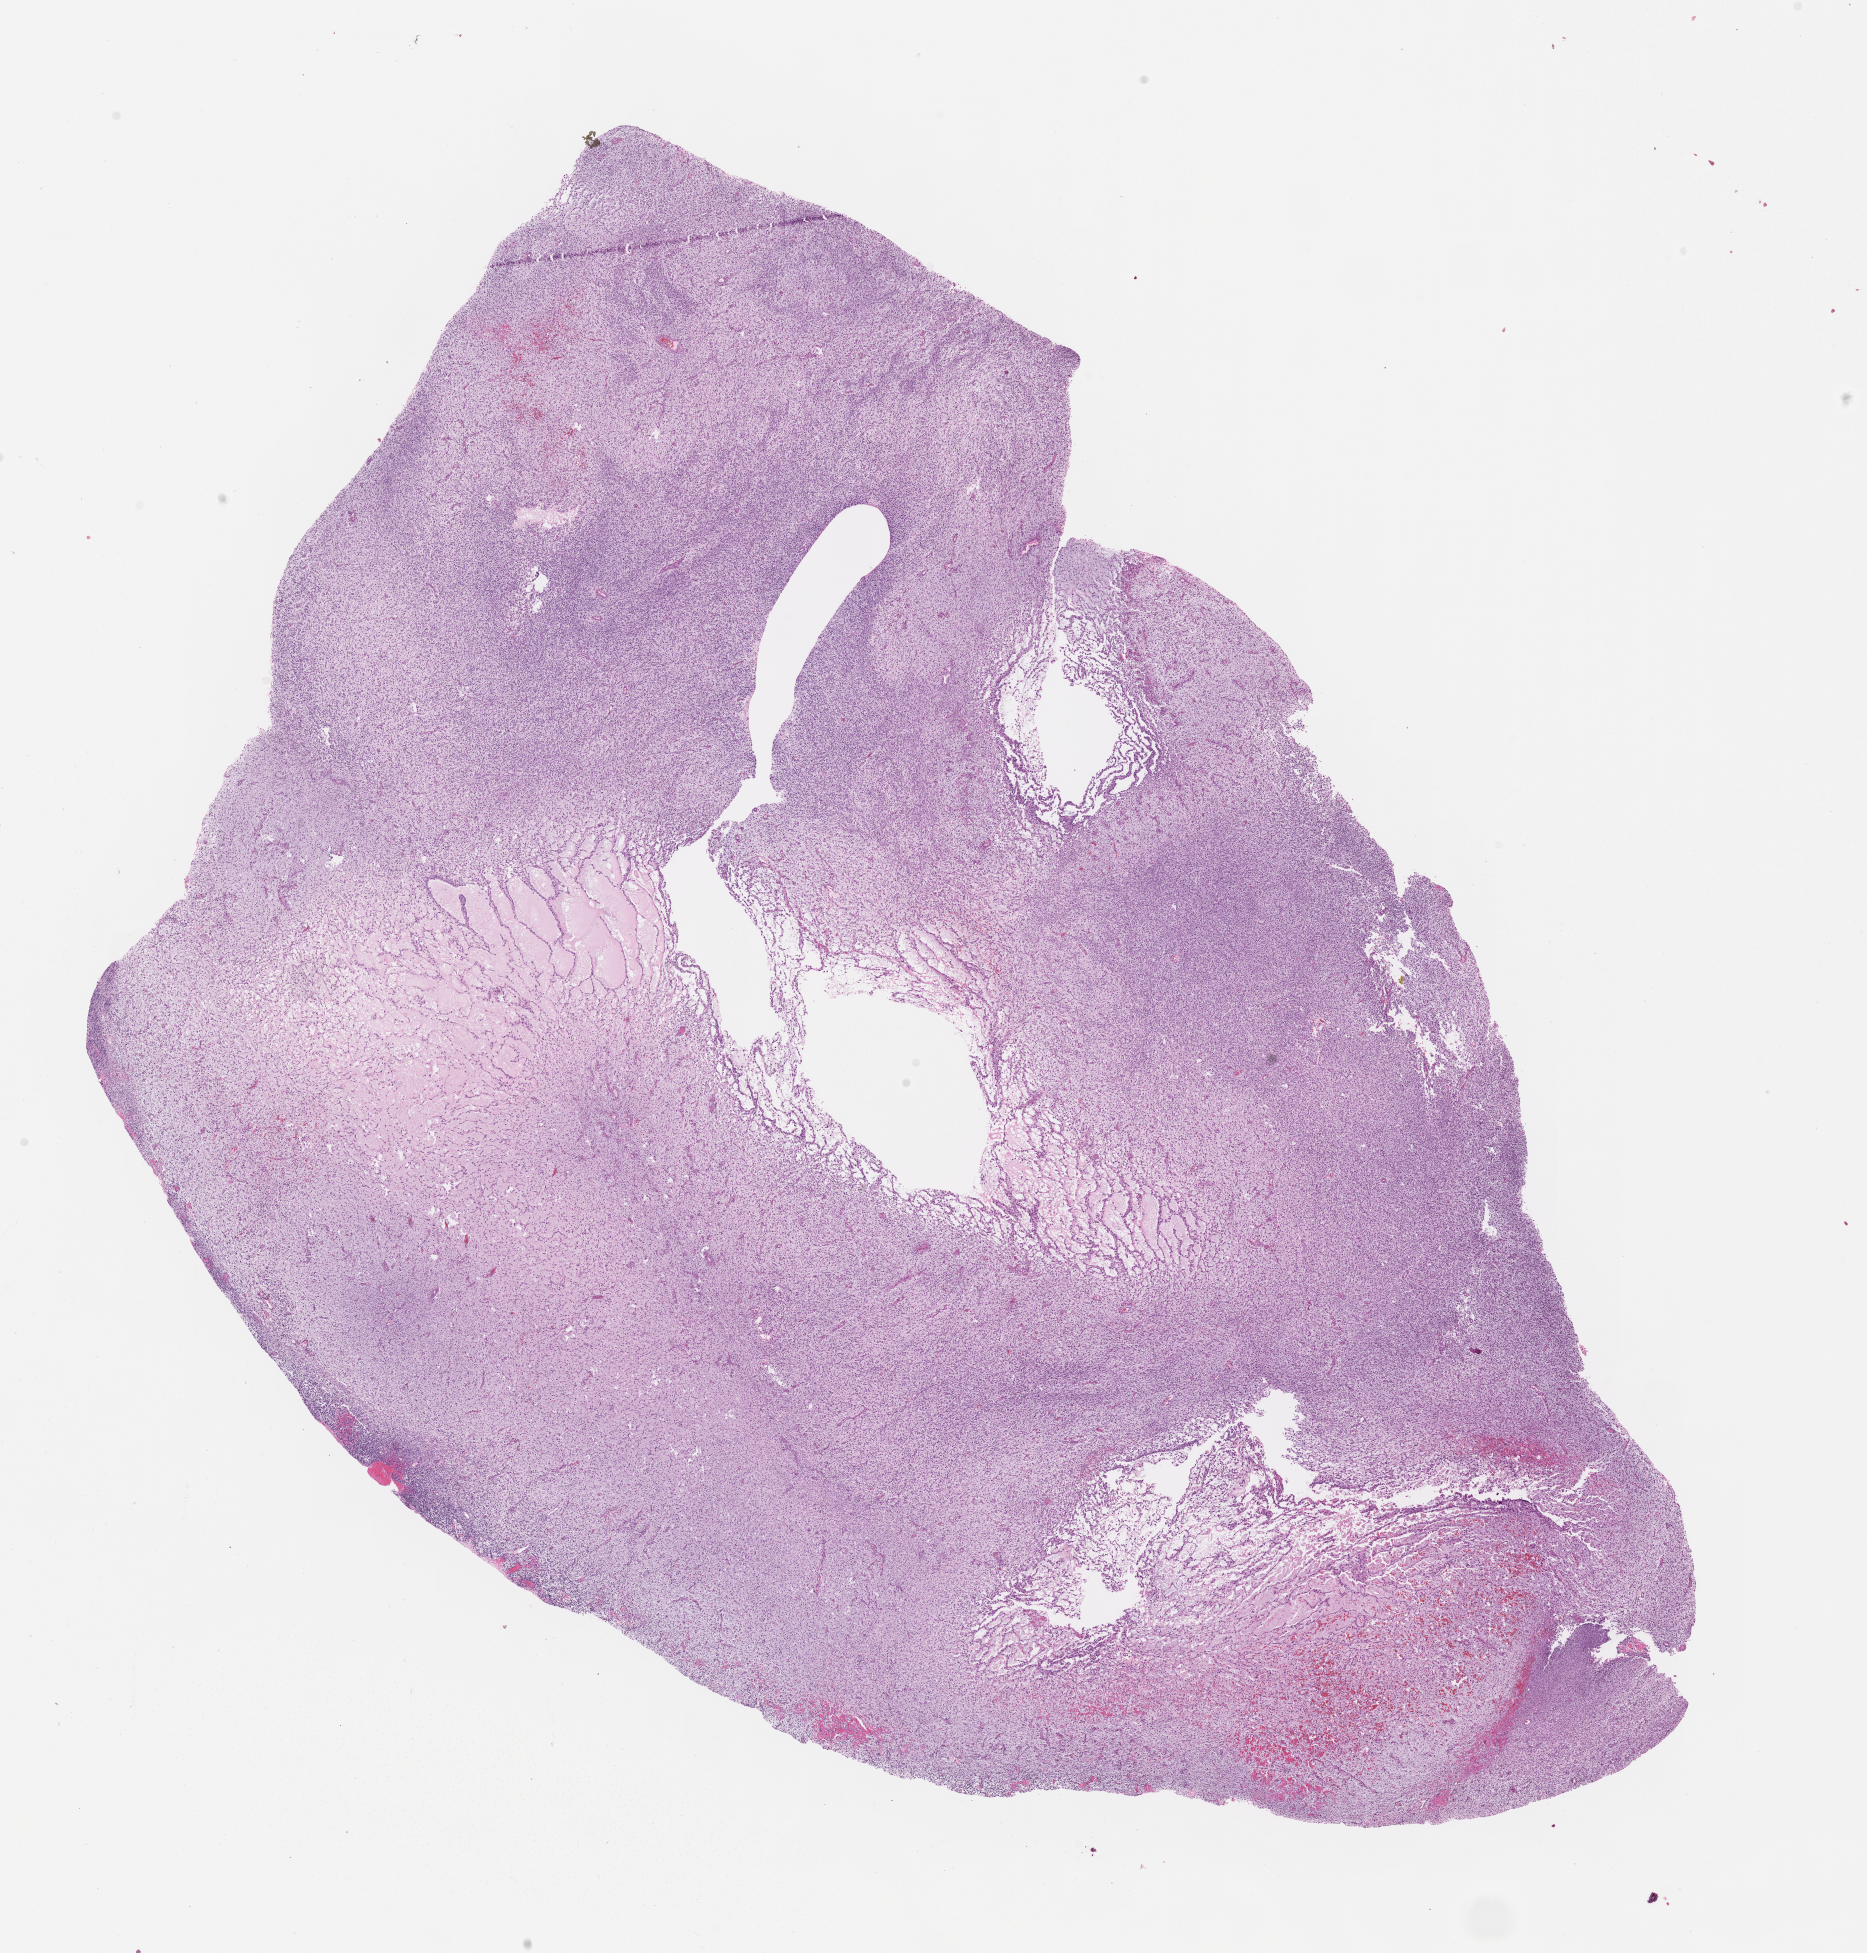
Digitized haematoxylin and eosin-stained section of tumor tissue — a low-resolution overview of the entire scanned area, about 15.1 x 15.8 mm; formalin-fixed, paraffin-embedded (FFPE) tissue; sample anatomic site: abdomen. Patient: female, age 3.2 years at diagnosis.
• stage (as recorded): 4
• metastatic status at presentation (as recorded): metastatic
• diagnosis: rhabdomyosarcoma; histological classification: embryonal rhabdomyosarcoma
• primary site (case record): abdominal Wall